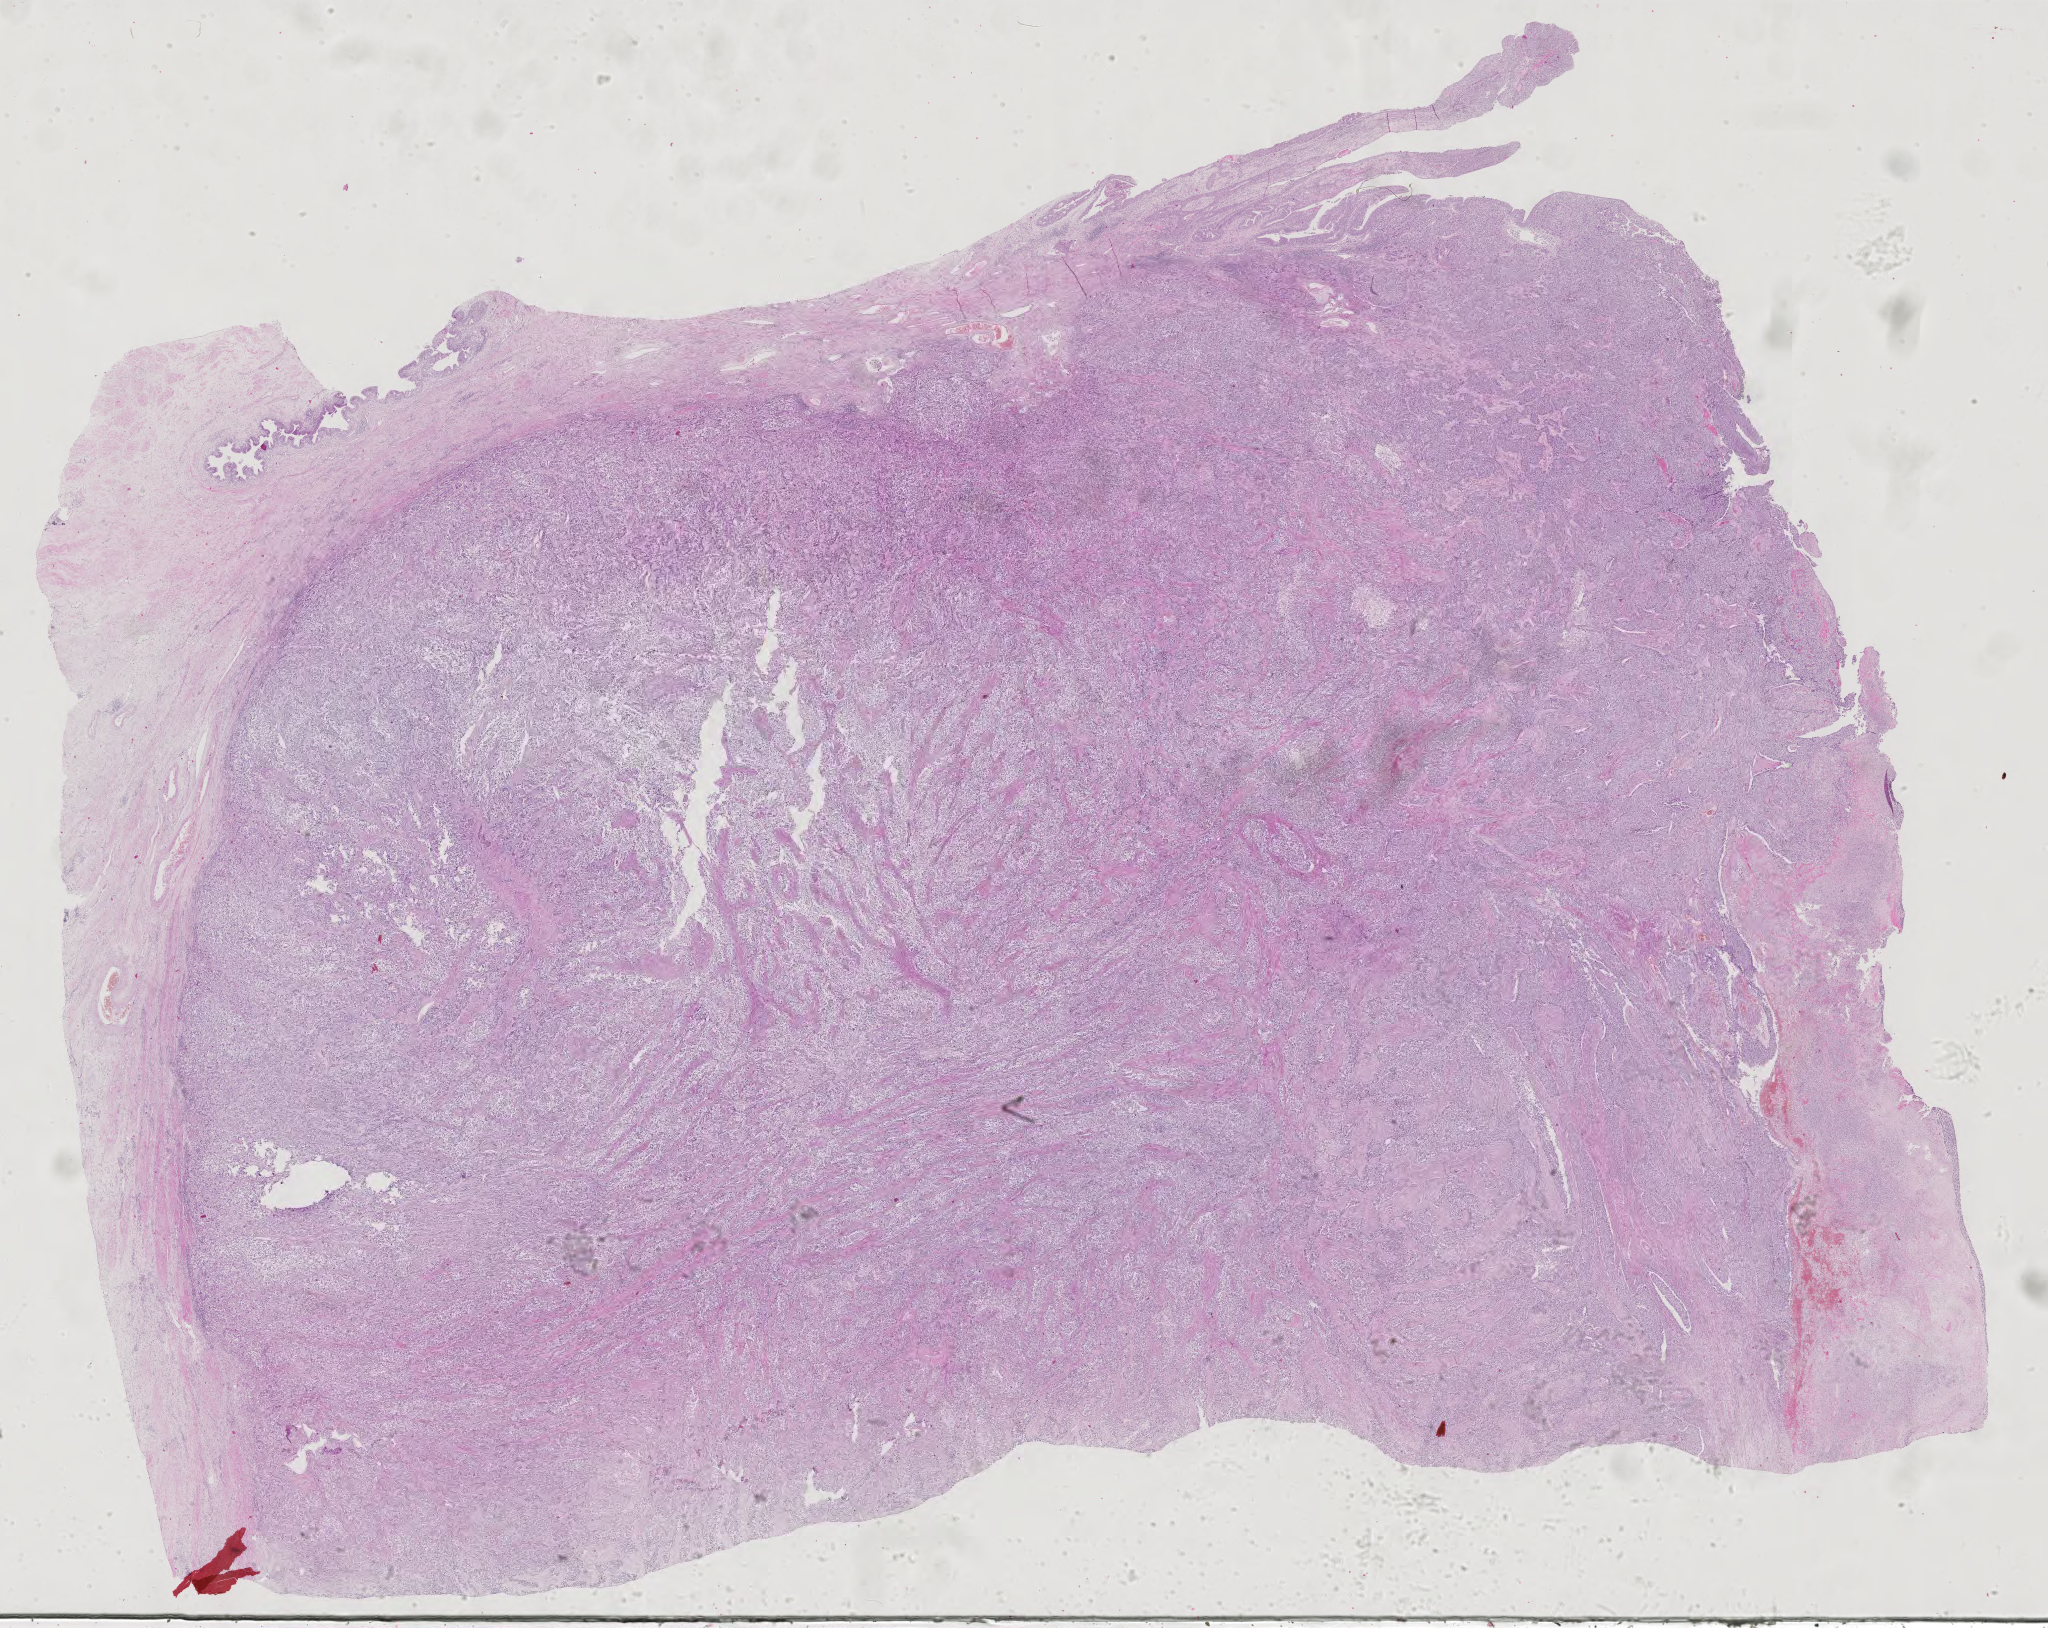
Whole-slide histology image, H&E-stained, a low-resolution overview of the entire scanned area, about 29.8 x 23.7 mm (from a 40x scan). Formalin-fixed paraffin-embedded (FFPE) diagnostic section. Bladder, primary tumour sample. Male patient. Histologic grade: high grade.
AJCC pathologic stage: II. Histologic diagnosis: Transitional cell carcinoma (posterior wall of bladder). Lymph nodes positive (case pathology): 0 of 20 examined.